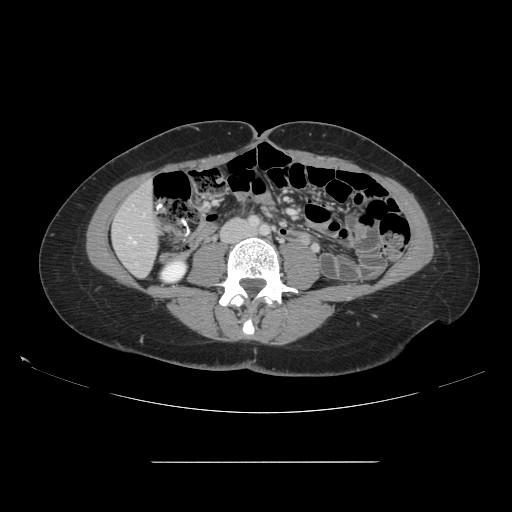
Contrast-enhanced abdominal CT, one axial slice. Slice 28 of 151 in the series (ordered by position). Intravenous contrast given. Soft-tissue window (W 400 / L 40 HU). 2.5 mm slice thickness. 512 × 512 image matrix. Female patient, age 46 years. Case-level facts recorded for this patient, not image findings: diagnosis: colorectal cancer liver metastases, imaged before liver resection; multiple liver metastases: yes; largest metastasis: 3 cm.
Annotated regions visible in this slice (outlined manually by an expert reader):
- hepatic veins: box from (x=133, y=241) to (x=135, y=243) px
- liver: (x=113, y=185)–(x=158, y=276)
- planned liver remnant (the part of the liver to remain after resection): (x=113, y=185)–(x=158, y=277)